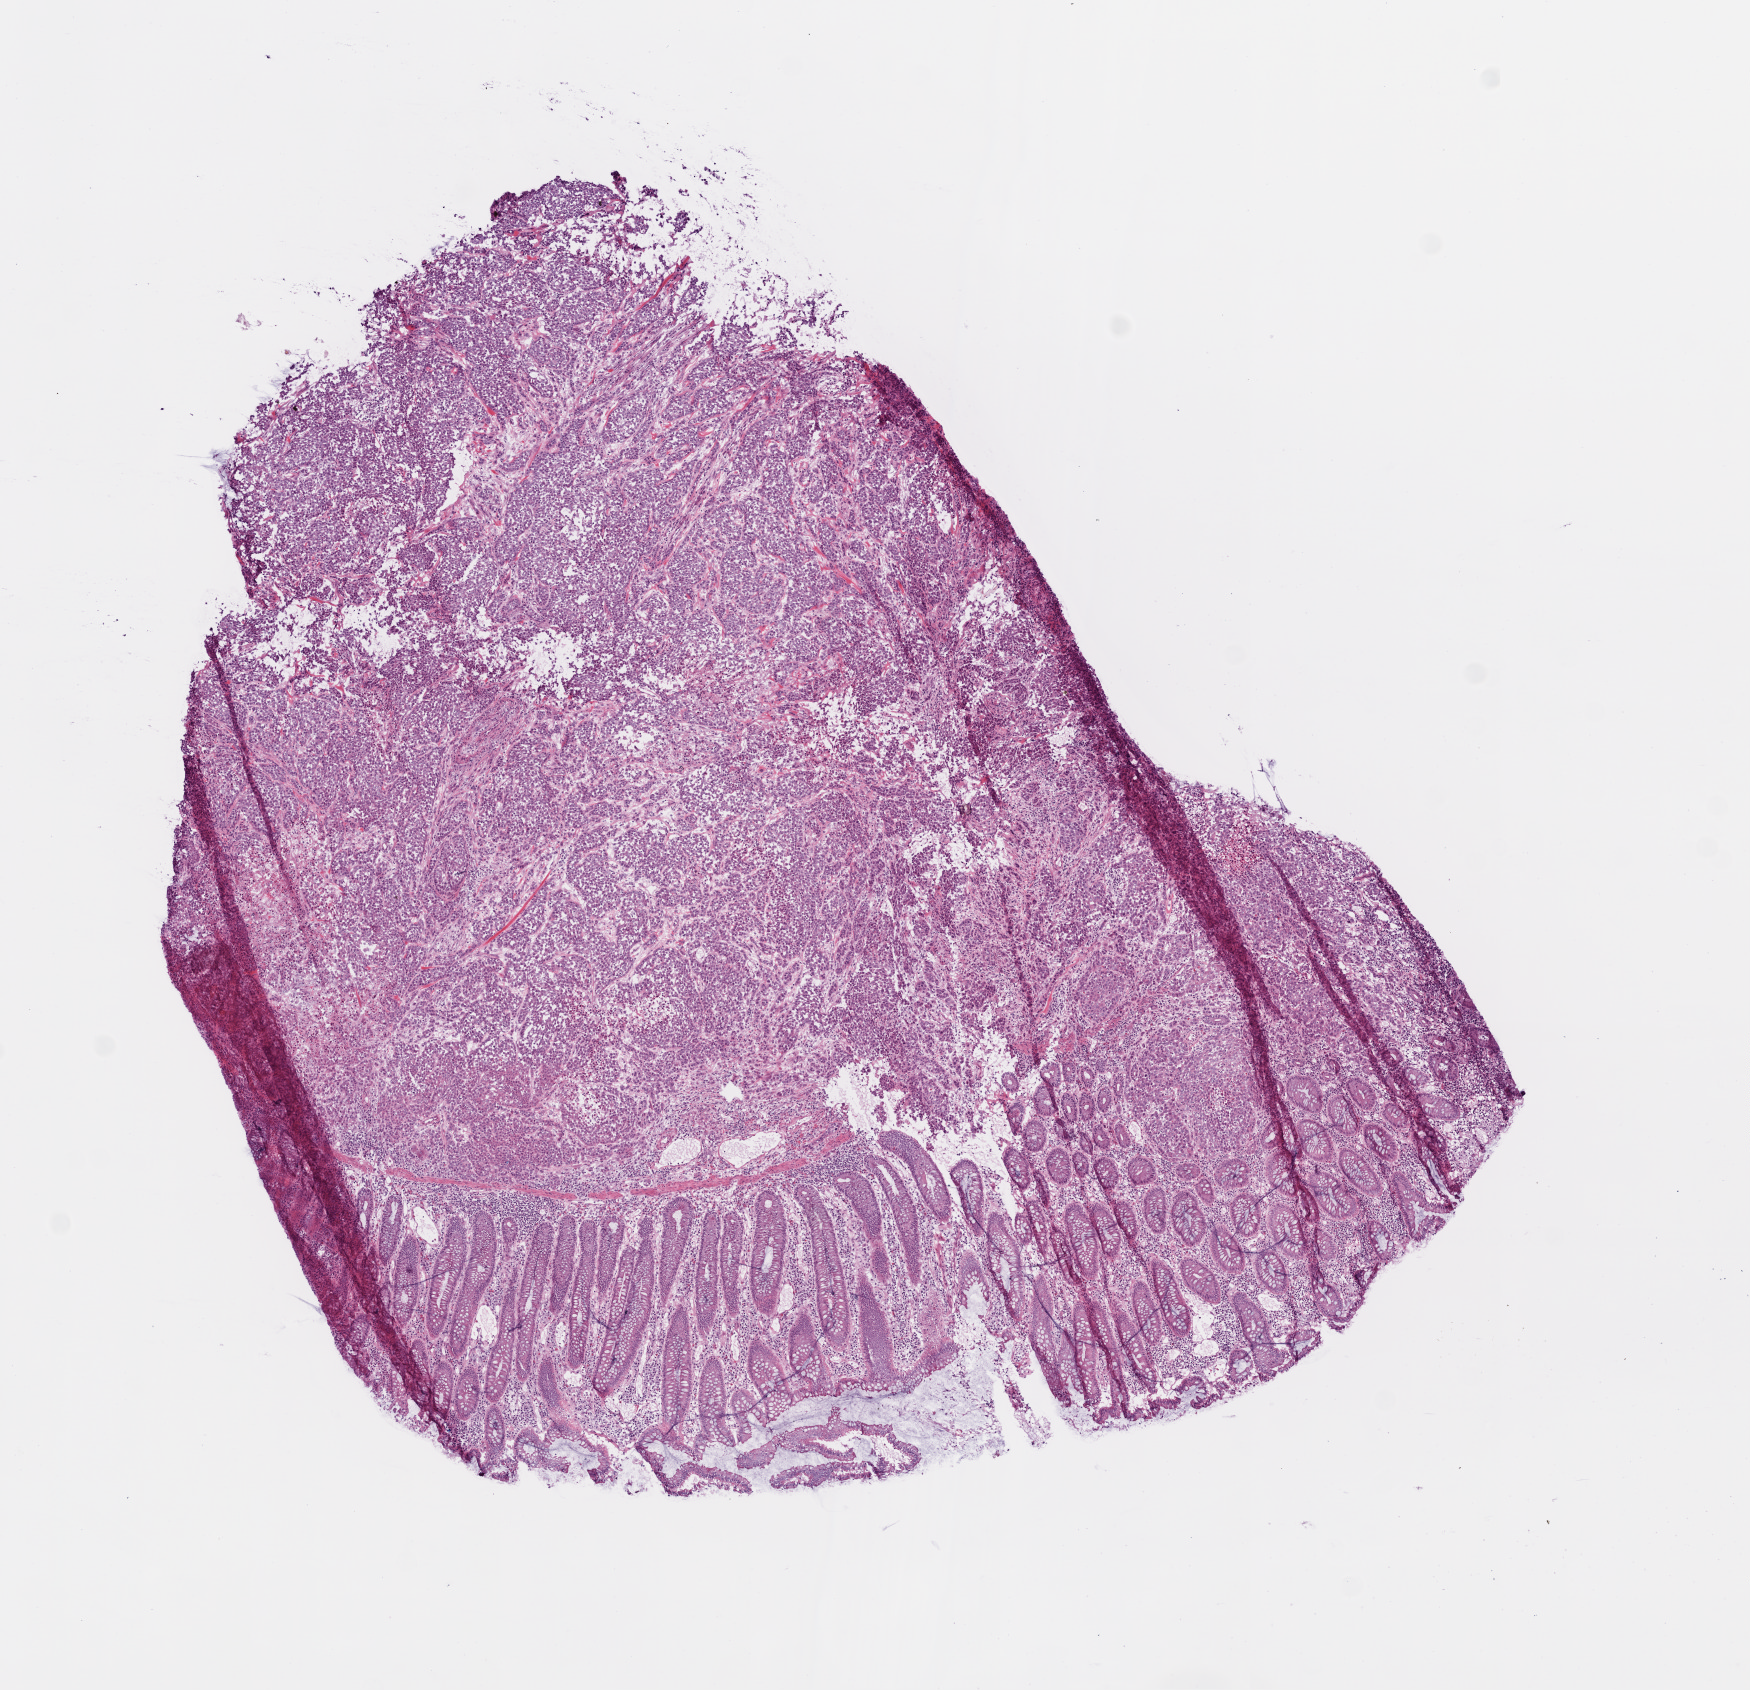
H&E-stained whole-slide image — a low-resolution overview of the entire scanned area, about 7.0 x 6.8 mm (acquisition: 20x scan); frozen section from the top of the tissue portion; colon, primary tumour sample. Patient: female, age at initial diagnosis 86 years. Slide review estimates, as recorded: tumour cells 74%, tumour nuclei 80%, normal cells 15%, stromal cells 8%, necrosis 3%.
• lymph nodes positive (case pathology): 0 of 12 examined
• AJCC pathologic stage: IIA (6th edition)
• histologic diagnosis: Adenocarcinoma, NOS (ascending colon)
• TNM: T3 N0 M0